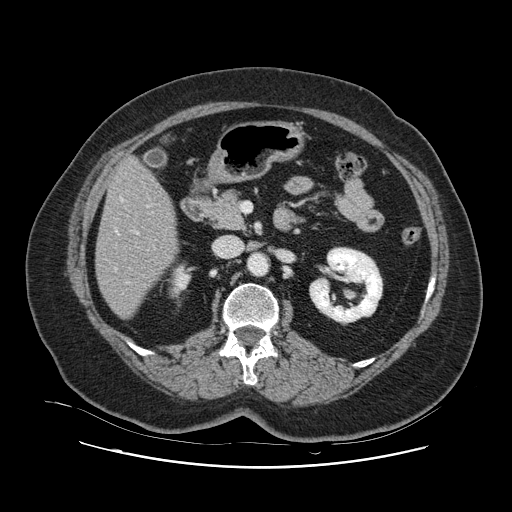
Contrast-enhanced abdominal CT, one axial slice; position 41 of 132 along the scan axis; 120 kVp; intravenous contrast given; soft-tissue window (W 400 / L 40 HU); 2.5 mm slice thickness; 512 × 512 image matrix, field of view 391 × 391 mm. Female patient, age 73 years. Case-level facts recorded for this patient, not image findings: diagnosis: colorectal cancer liver metastases, imaged before liver resection; multiple liver metastases: no; largest metastasis: 7 cm; chemotherapy before resection: yes.
Annotated regions visible in this slice (expert manual segmentation):
- hepatic veins: bounding box [x1, y1, x2, y2] px = [115, 199, 153, 271]
- liver: [97, 159, 178, 318]
- planned liver remnant (the part of the liver to remain after resection): [97, 159, 178, 318]
- portal vein (with intrahepatic branches): [128, 231, 139, 283]